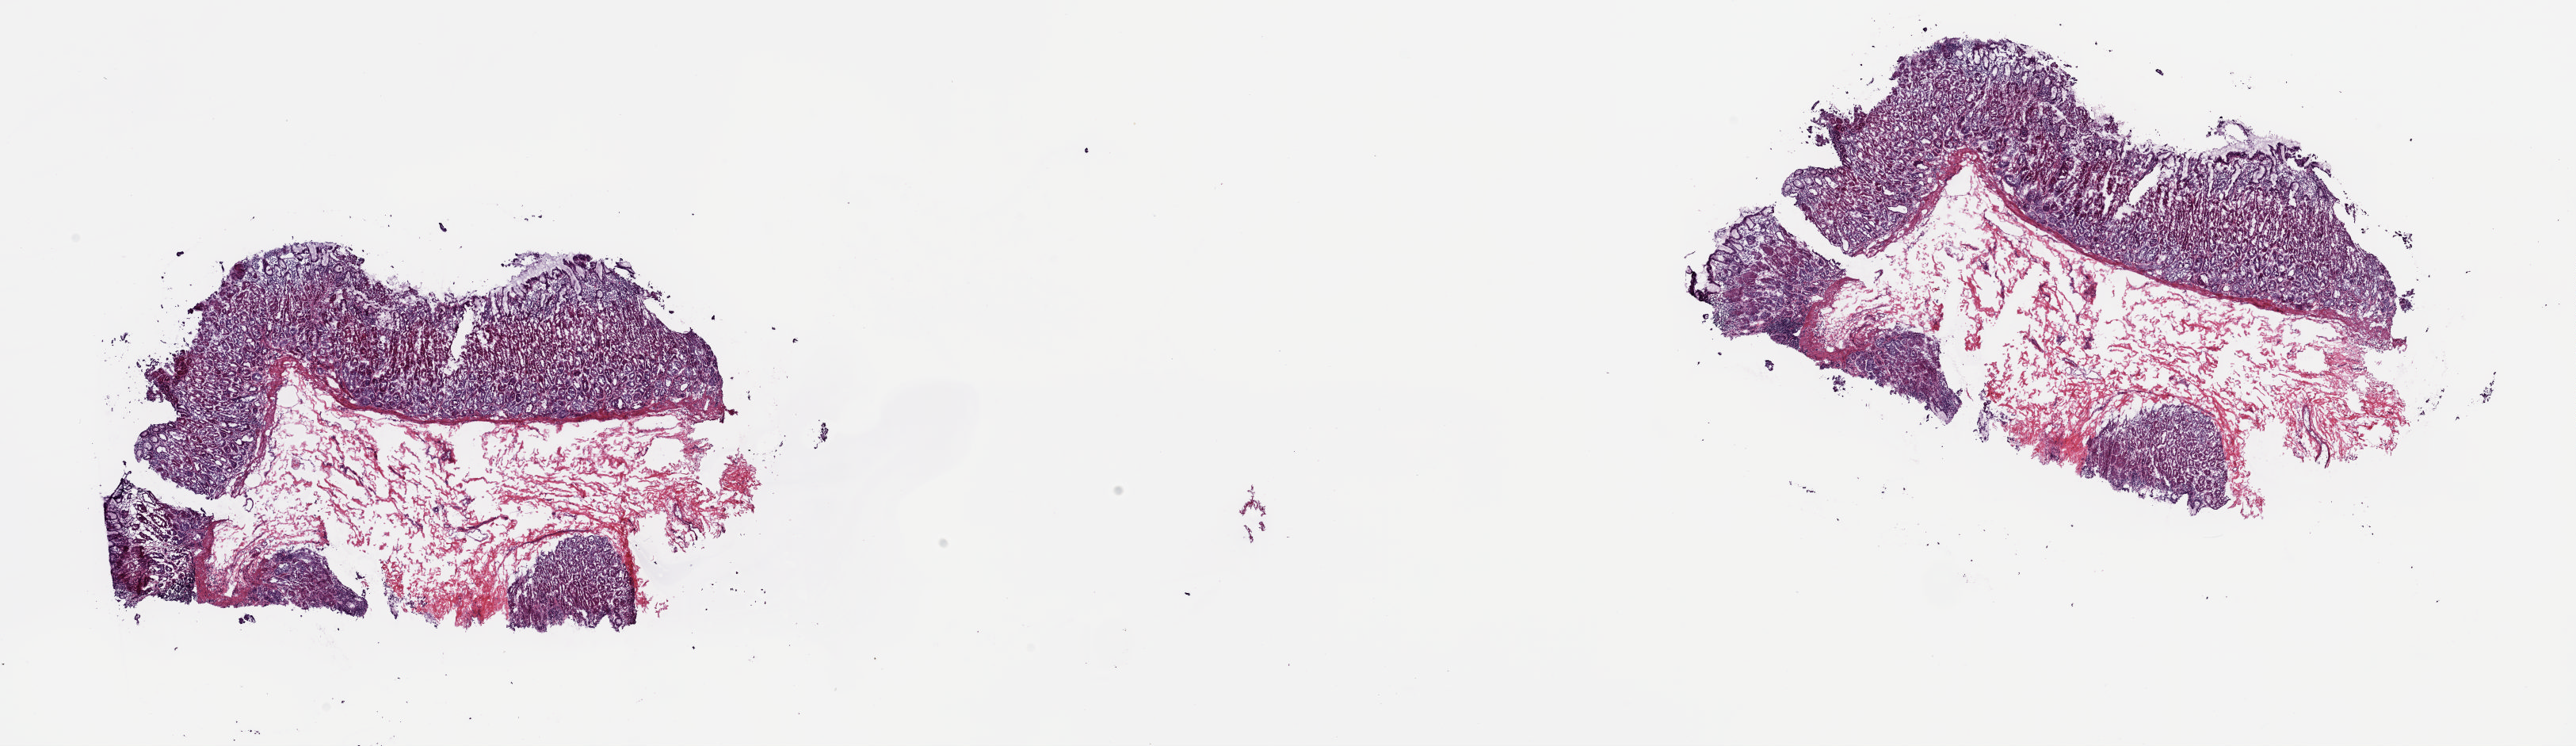
Whole-slide histology image, H&E-stained, whole scanned area (about 25.8 x 7.5 mm, acquisition: 20x scan) shown as a low-resolution overview; frozen section from the top of the tissue portion; esophagus, solid tissue normal (non-tumour tissue) sample. Male patient; age at initial diagnosis 66 years. Pathologist review of this section (percent, as recorded): tumour cells 0%, tumour nuclei 0%, normal cells 100%, stromal cells 0%, necrosis 0%. Inflammatory infiltration, as recorded: lymphocyte infiltration 0%, monocyte infiltration 0%, neutrophil infiltration 0%.
This section: solid tissue normal (non-tumour) sample from the same patient. Patient diagnosis: Adenocarcinoma, NOS.